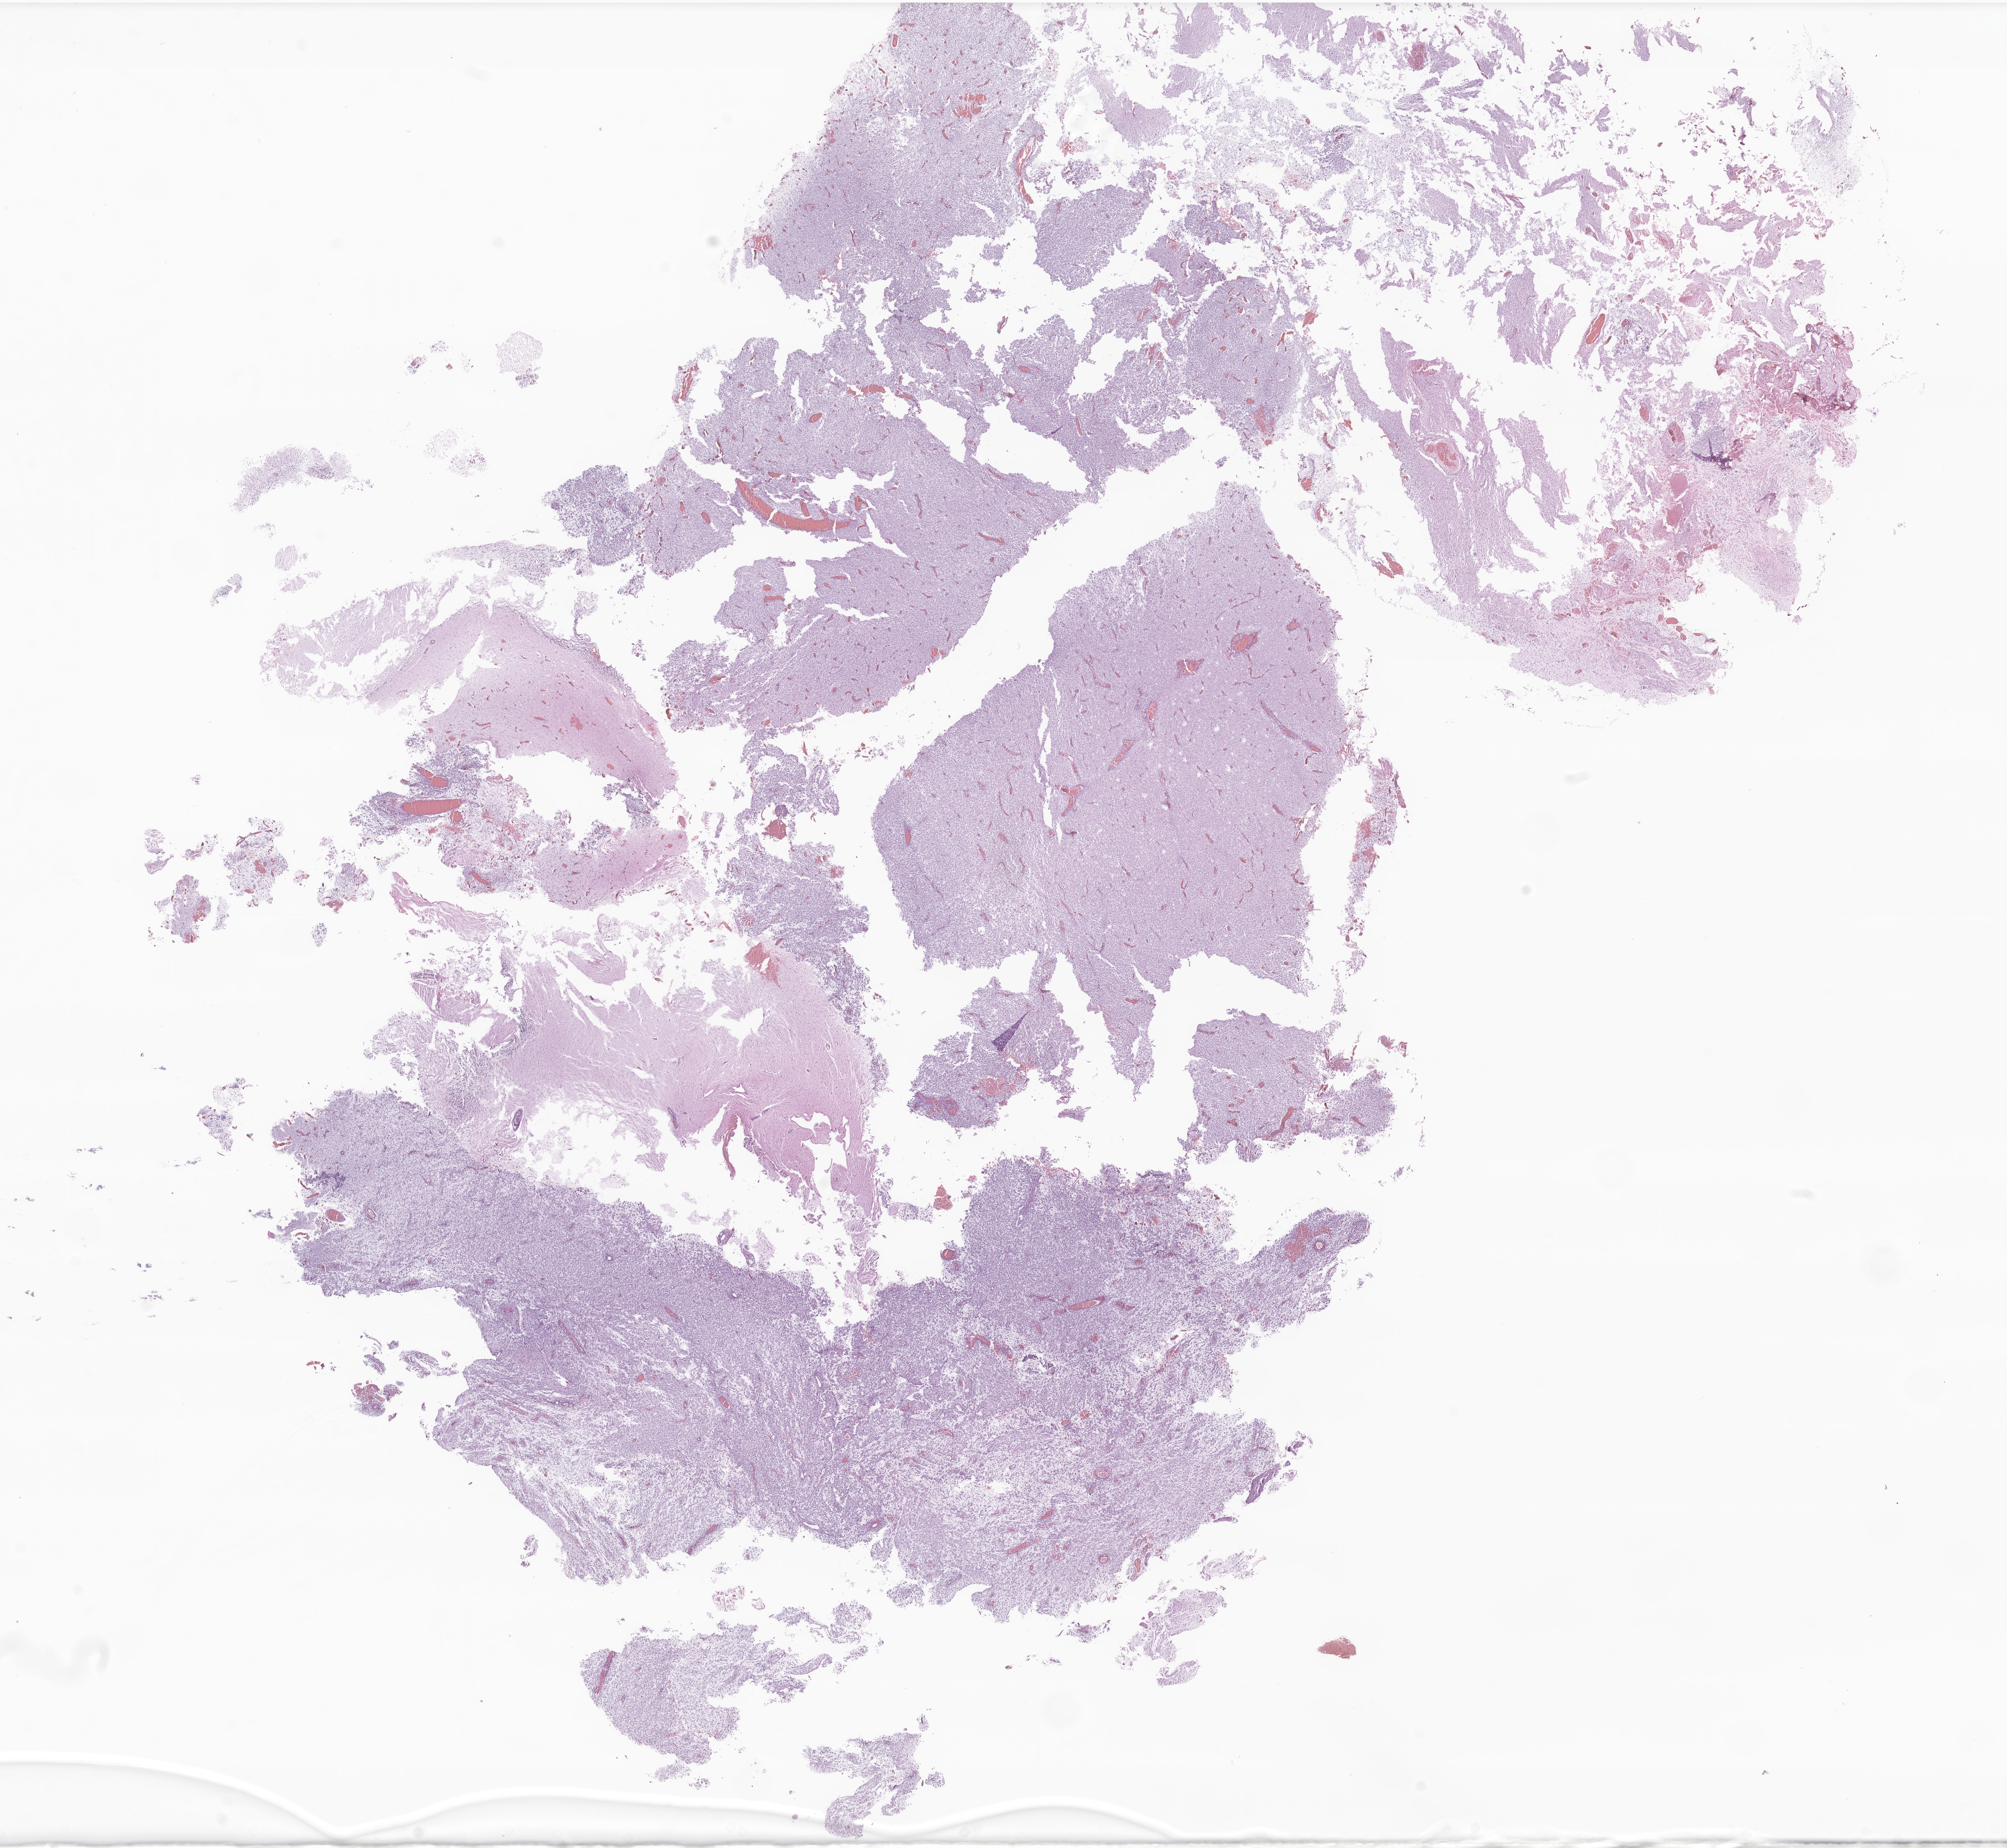
Digitized H&E-stained section of tumor tissue from the brain — a low-resolution overview of the entire scanned area, about 25.2 x 23.2 mm, formalin-fixed, paraffin-embedded (FFPE) tissue. Patient male; age 752 days (about 2.1 years).
* recorded diagnosis: Pilocytic astrocytoma